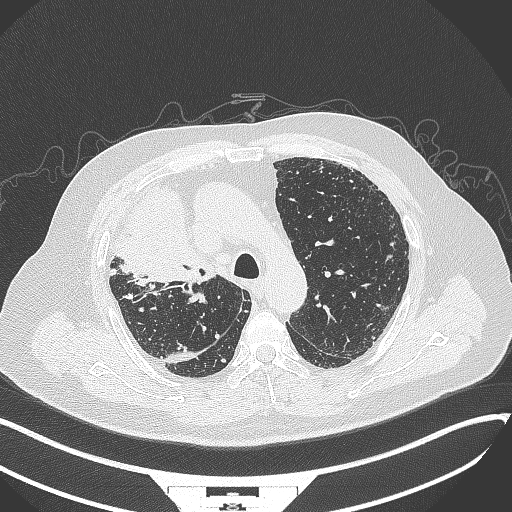
Chest CT, one axial slice. Slice 252 of 384 in the series (ordered by position). Reconstruction kernel B70f. Lung window (W 1500 / L -600 HU). 512 × 512 image matrix, field of view 400 × 400 mm. Male patient, age 69 years. From the clinical record (not read from this slice): clinical TNM (as recorded): T4 N3 M1.
Structures marked on this image (bounding box drawn by a radiologist):
- lung tumour (recorded histology: adenocarcinoma): box from (x=113, y=177) to (x=212, y=286) px